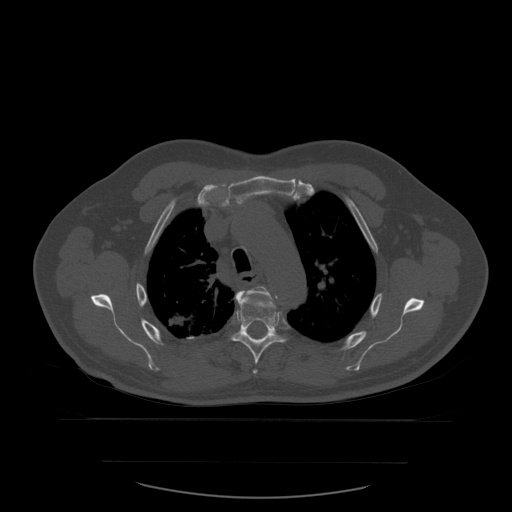
CT including the spine, one axial slice; position 426 of 590 along the scan axis; bone window (W 1800 / L 400 HU); 1.25 mm slice thickness; 512 × 512 image matrix. Patient age 71 years. Case-level facts recorded for this patient, not image findings: primary cancer: lung.
Annotated regions visible in this slice (semi-automatically segmented with operator editing):
- T4 vertebra: bounding box [x1, y1, x2, y2] px = [243, 287, 272, 374]
- T5 vertebra: [230, 291, 287, 365]
- T6 vertebra: [251, 334, 268, 340]